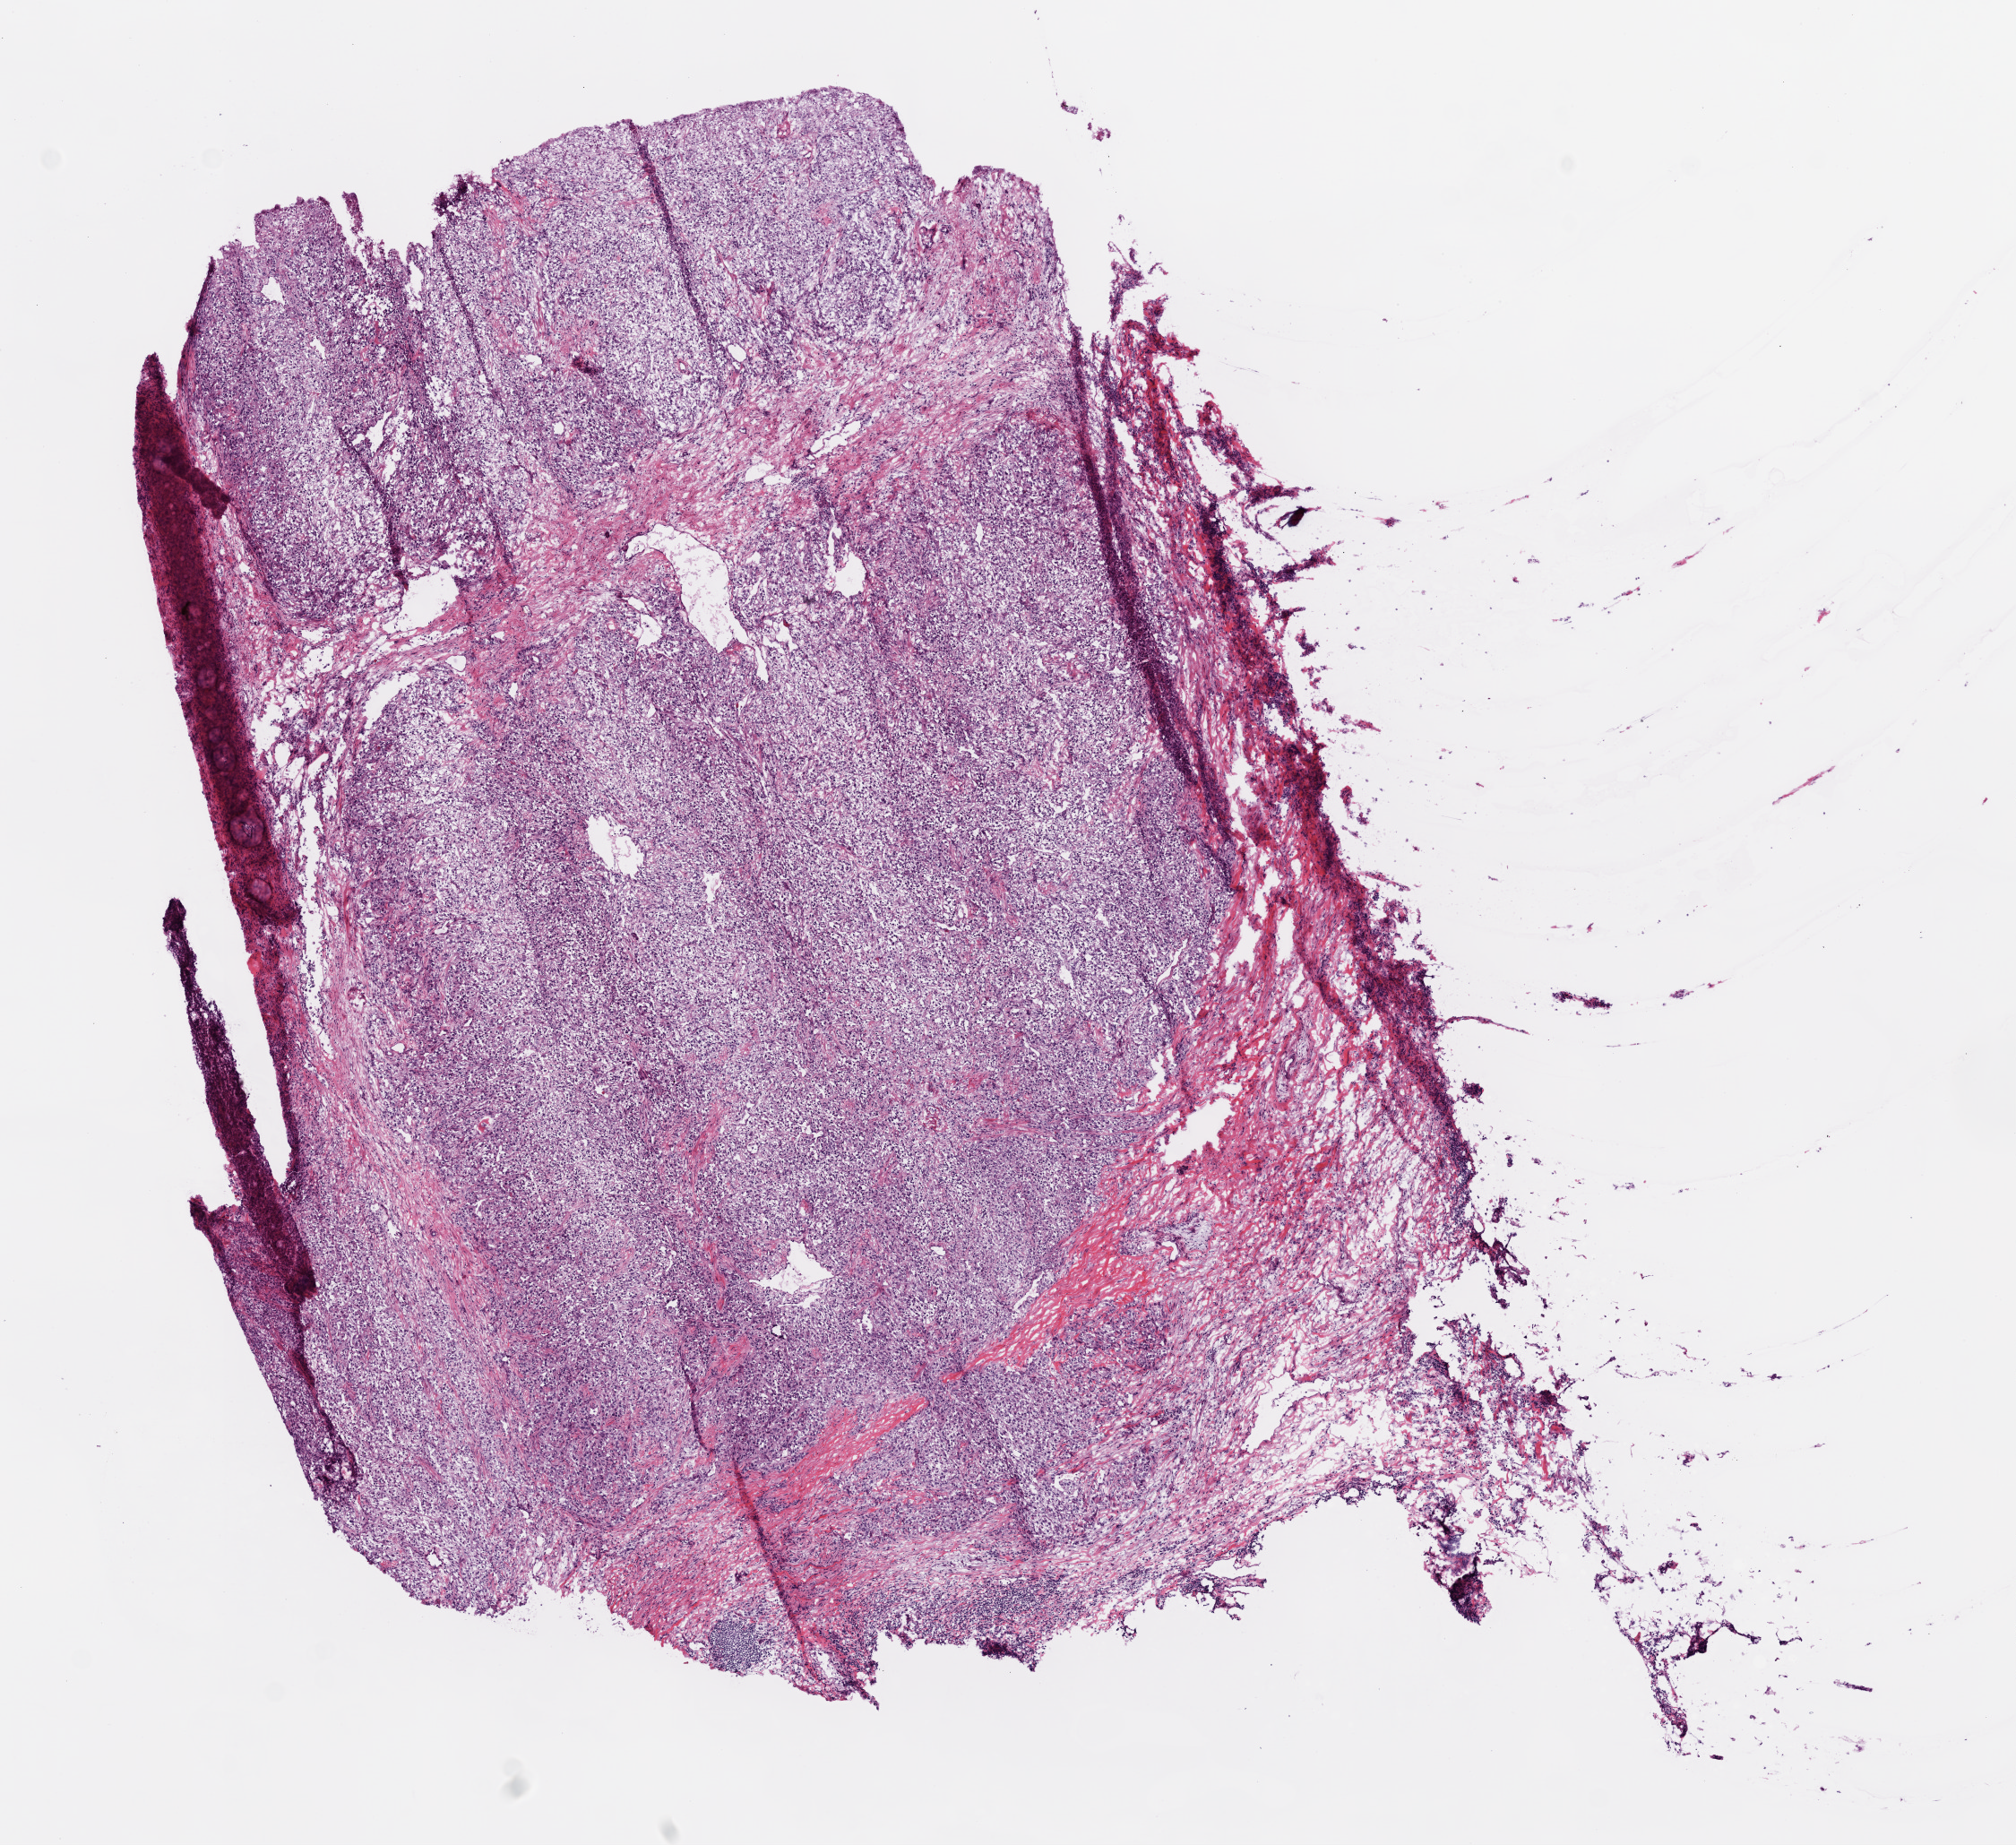
H&E-stained whole-slide image, shown as a low-resolution overview of the whole scanned area (about 9.0 x 8.3 mm, from a 20x scan); frozen section from the top of the tissue portion; sample: primary tumour, kidney. Patient: female, age at initial diagnosis 76 years. Histologic grade: G2 (moderately differentiated). Composition of this section per pathologist review: tumour cells 90%, tumour nuclei 80%, normal cells 0%, stromal cells 10%, necrosis 0%. Infiltration values recorded for this section: lymphocyte infiltration 15%, monocyte infiltration 1%, neutrophil infiltration 0%.
Lymph nodes positive (case pathology): 1 of 1 examined. Histologic diagnosis: Clear cell adenocarcinoma, NOS. AJCC pathologic stage: III.